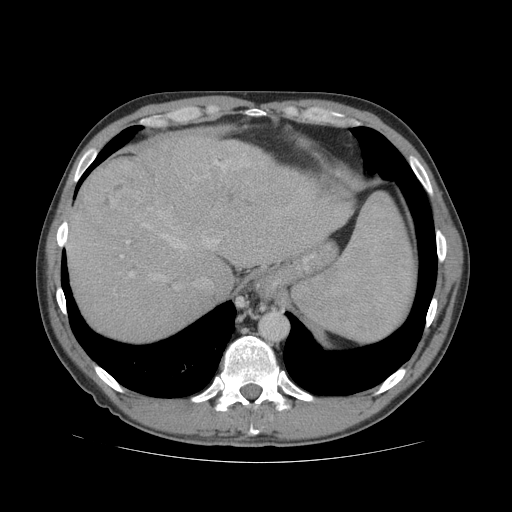
Contrast-enhanced abdominal CT (liver protocol), one axial slice; reconstruction kernel STANDARD; 140 kVp; soft-tissue window (W 400 / L 40 HU); 2.5 mm slice thickness; 512 × 512 image matrix. Case-level facts recorded for this patient, not image findings: diagnosis: hepatocellular carcinoma (patient treated with transarterial chemoembolisation; whether this scan precedes or follows treatment is not stated here); TNM stage (as recorded): Stage-IVB; Child-Pugh class: B; tumour differentiation: well differentiated; tumour nodularity: multinodular.
Annotated regions visible in this slice (semi-automatic segmentation, software-assisted and operator-edited):
- abdominal aorta: bounding box (x1, y1, x2, y2) in pixels: (260, 313, 288, 339)
- liver parenchyma outside the tumour (the mass and vessels are separate outlines, so this box may not span the whole liver): (66, 134, 352, 340)
- mass: (78, 132, 265, 233)
- liver vessels: (69, 211, 220, 279)